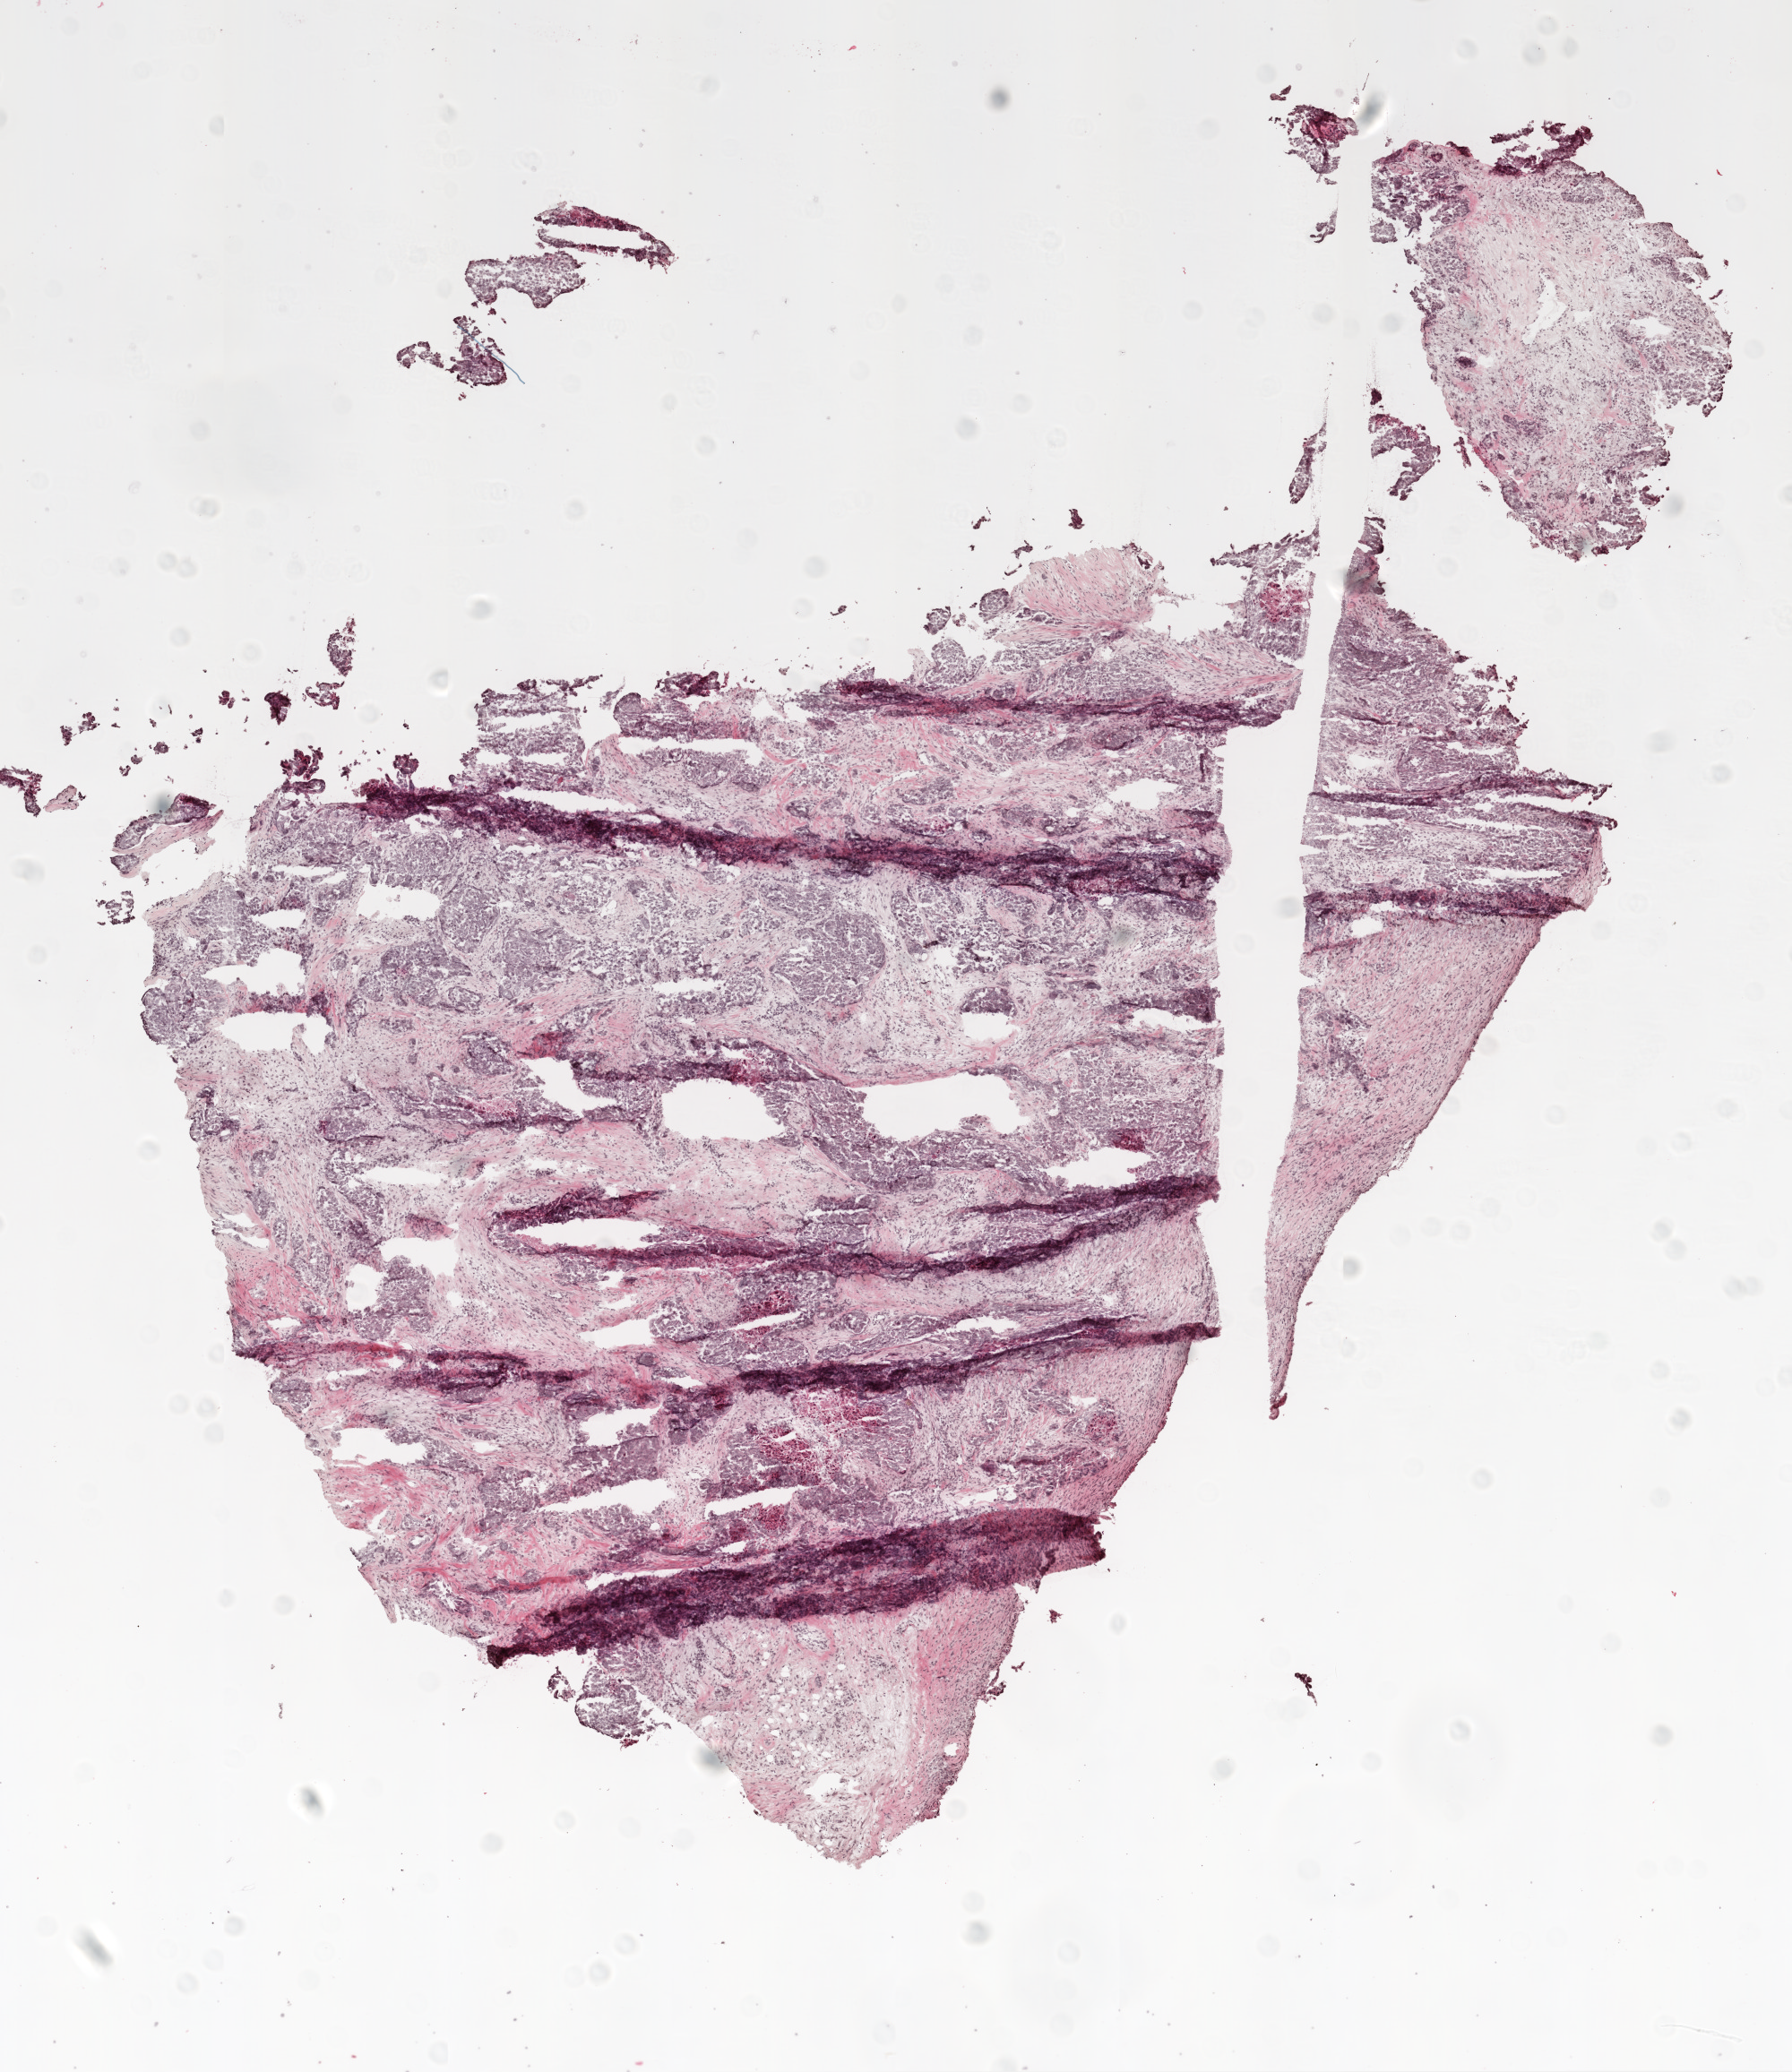
Digitized Hematoxylin and eosin (H&E) stained tissue section (whole slide) — whole scanned area (about 8.0 x 9.3 mm) shown as a low-resolution overview. Frozen section from the top of the tissue portion. Ovary, primary tumour sample. Female patient; age at initial diagnosis 52 years. Histologic grade: G3 (poorly differentiated). Pathologist review of this section (percent, as recorded): tumour cells 80%, tumour nuclei 90%, normal cells 0%, stromal cells 10%, necrosis 10%.
- FIGO stage: IIIC
- pathologic diagnosis: Serous cystadenocarcinoma, NOS